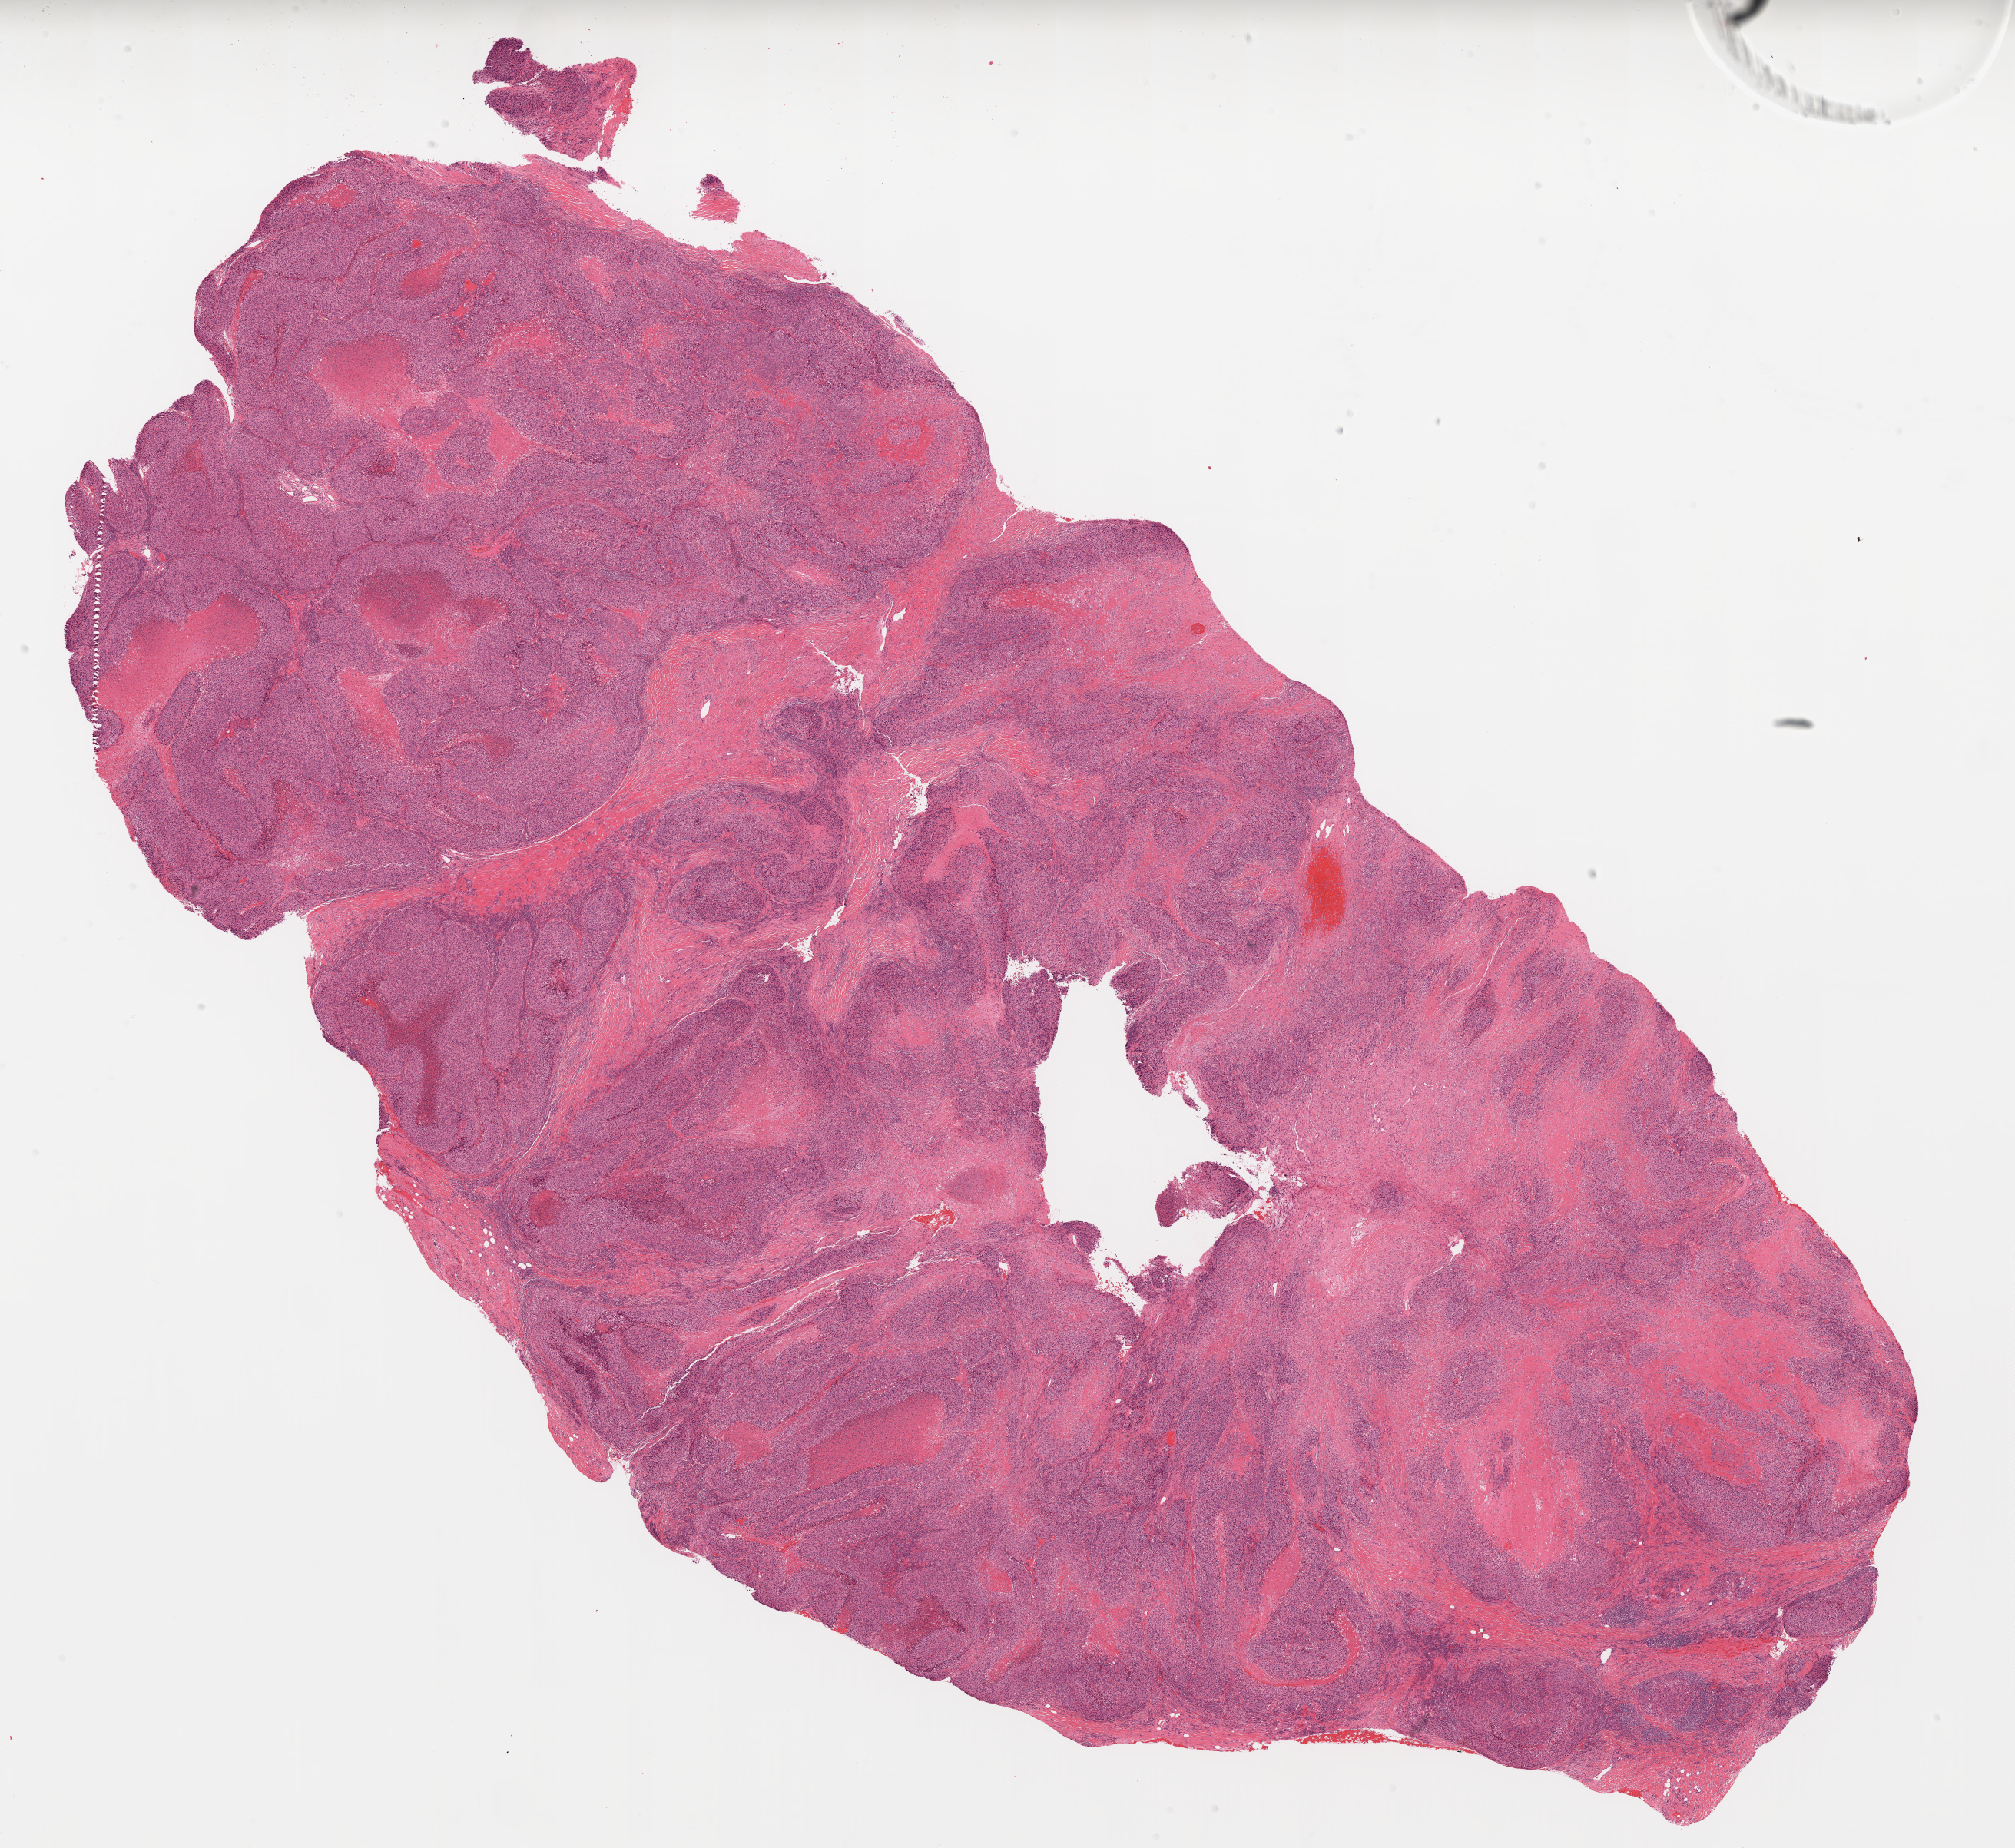
Digitized H&E-stained tissue section (whole slide), shown as a low-resolution overview of the whole scanned area (about 21.0 x 19.3 mm, acquisition: 20x scan); formalin-fixed paraffin-embedded (FFPE) diagnostic section; primary tumour sample from the skin. Female patient; age at initial diagnosis 59 years.
• histologic diagnosis: Malignant melanoma, NOS